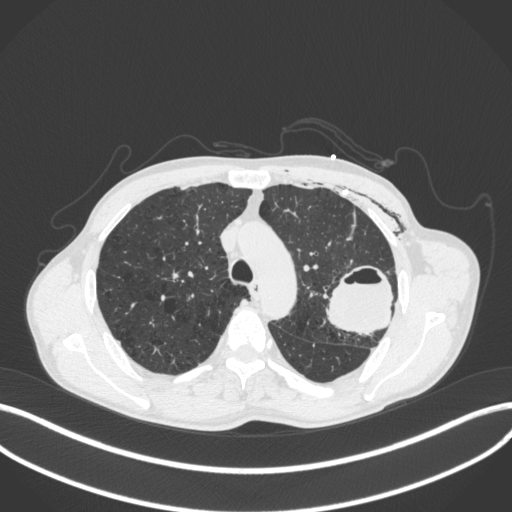
Chest CT, one axial slice. Position 294 of 416 along the scan axis. 120 kVp. Lung window (W 1500 / L -600 HU). 1 mm slice thickness. 512 × 512 image matrix, field of view 400 × 400 mm. Patient: male, 58 years. From the clinical record (not read from this slice): clinical TNM (as recorded): T3 N0 M0.
Outlined on this slice (bounding box drawn by a radiologist):
- lung tumour (recorded histology: adenocarcinoma): box from (x=324, y=259) to (x=398, y=343) px